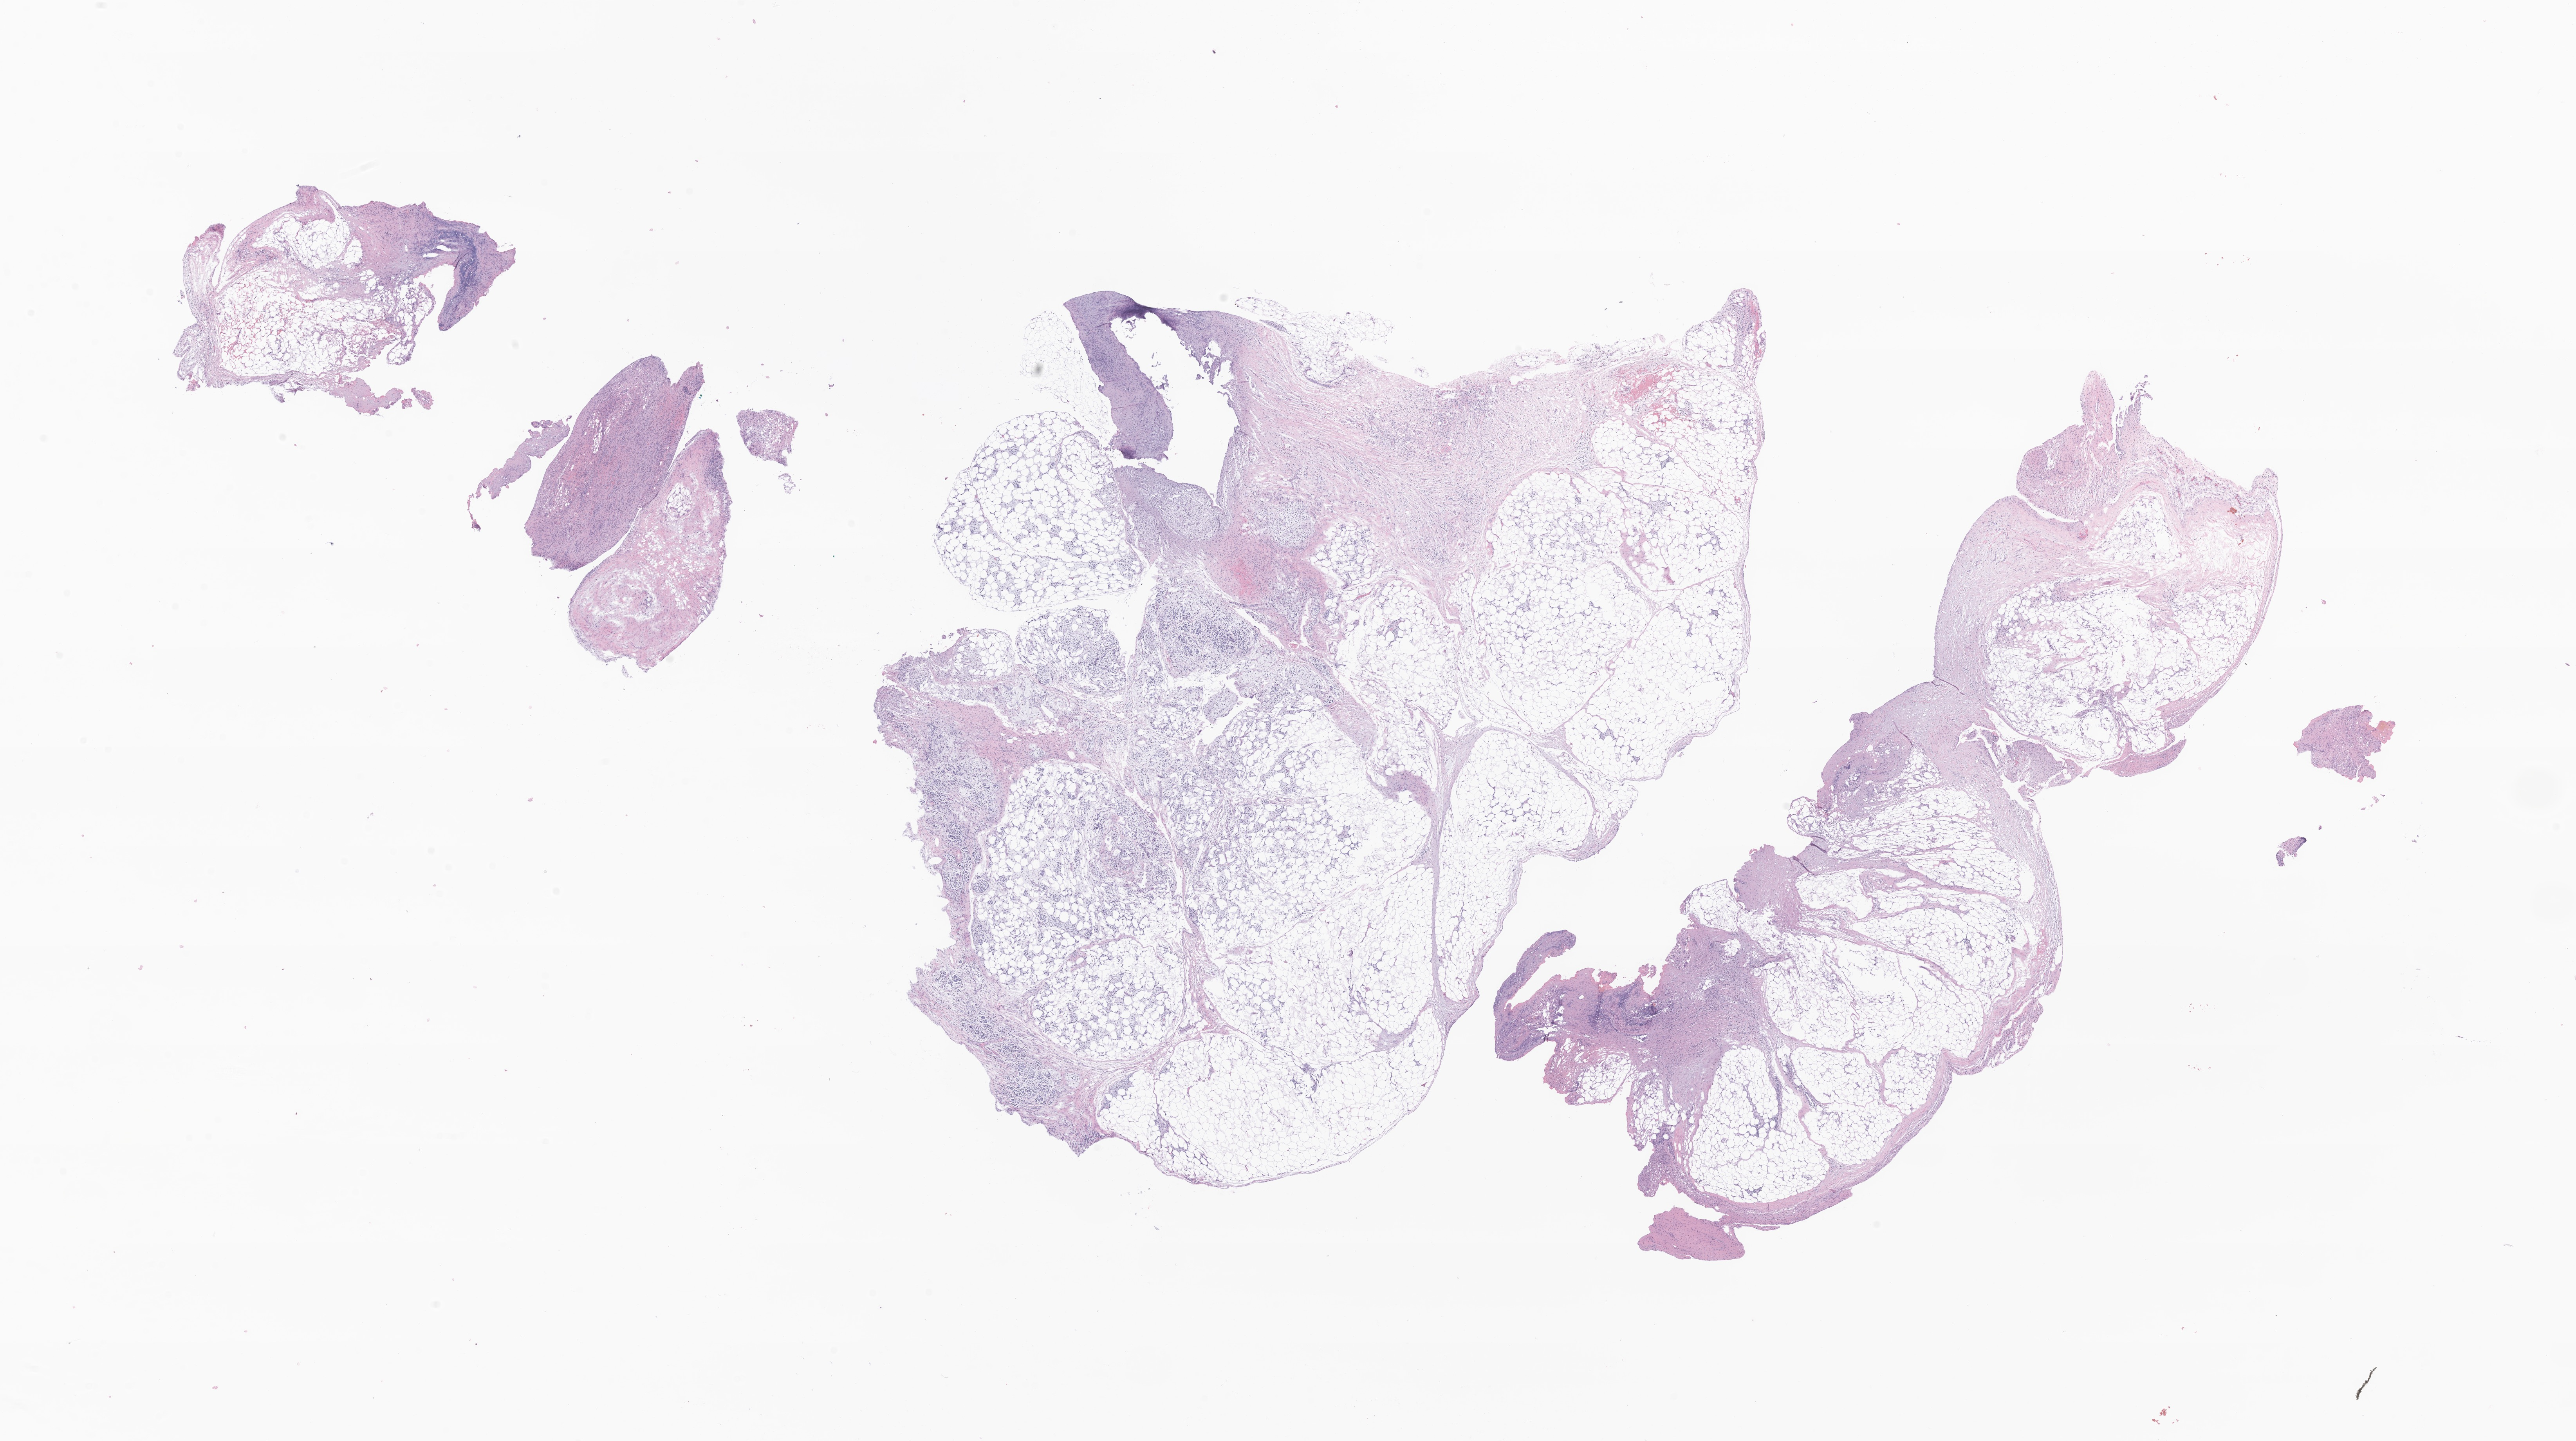
Digitized haematoxylin and eosin-stained section of tumor tissue from the gastrointestinal tract, a low-resolution overview of the entire scanned area, about 27.7 x 15.5 mm; formalin-fixed, paraffin-embedded (FFPE) tissue. Patient male; age 107 months (8 years 11 months).
Diagnosis: Metastatic signet ring cell carcinoma.